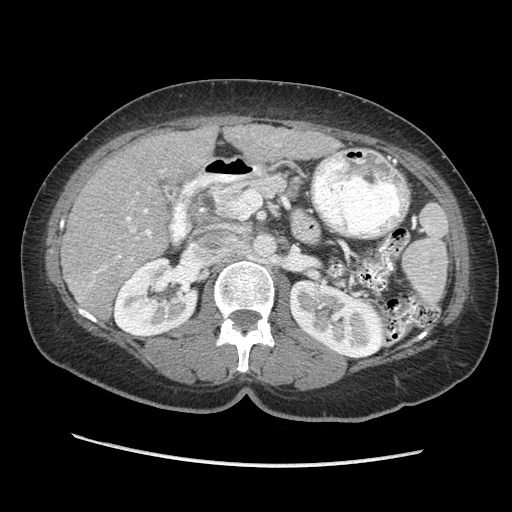
Contrast-enhanced abdominal CT (liver protocol), one axial slice; reconstruction kernel STANDARD; 140 kVp; soft-tissue window (W 400 / L 40 HU); 2.5 mm slice thickness; 512 × 512 image matrix, field of view 360 × 360 mm. Case-level facts recorded for this patient, not image findings: diagnosis: hepatocellular carcinoma (patient treated with transarterial chemoembolisation; whether this scan precedes or follows treatment is not stated here); TNM stage (as recorded): Stage-II; Child-Pugh class: A; tumour differentiation: no biopsy; tumour nodularity: multinodular.
Structures marked on this image (semi-automatic segmentation, software-assisted and operator-edited):
- liver parenchyma outside the tumour (the mass and vessels are separate outlines, so this box may not span the whole liver): bounding box <60,122,340,318> (left, top, right, bottom; pixels)
- liver vessels: <88,170,164,287>